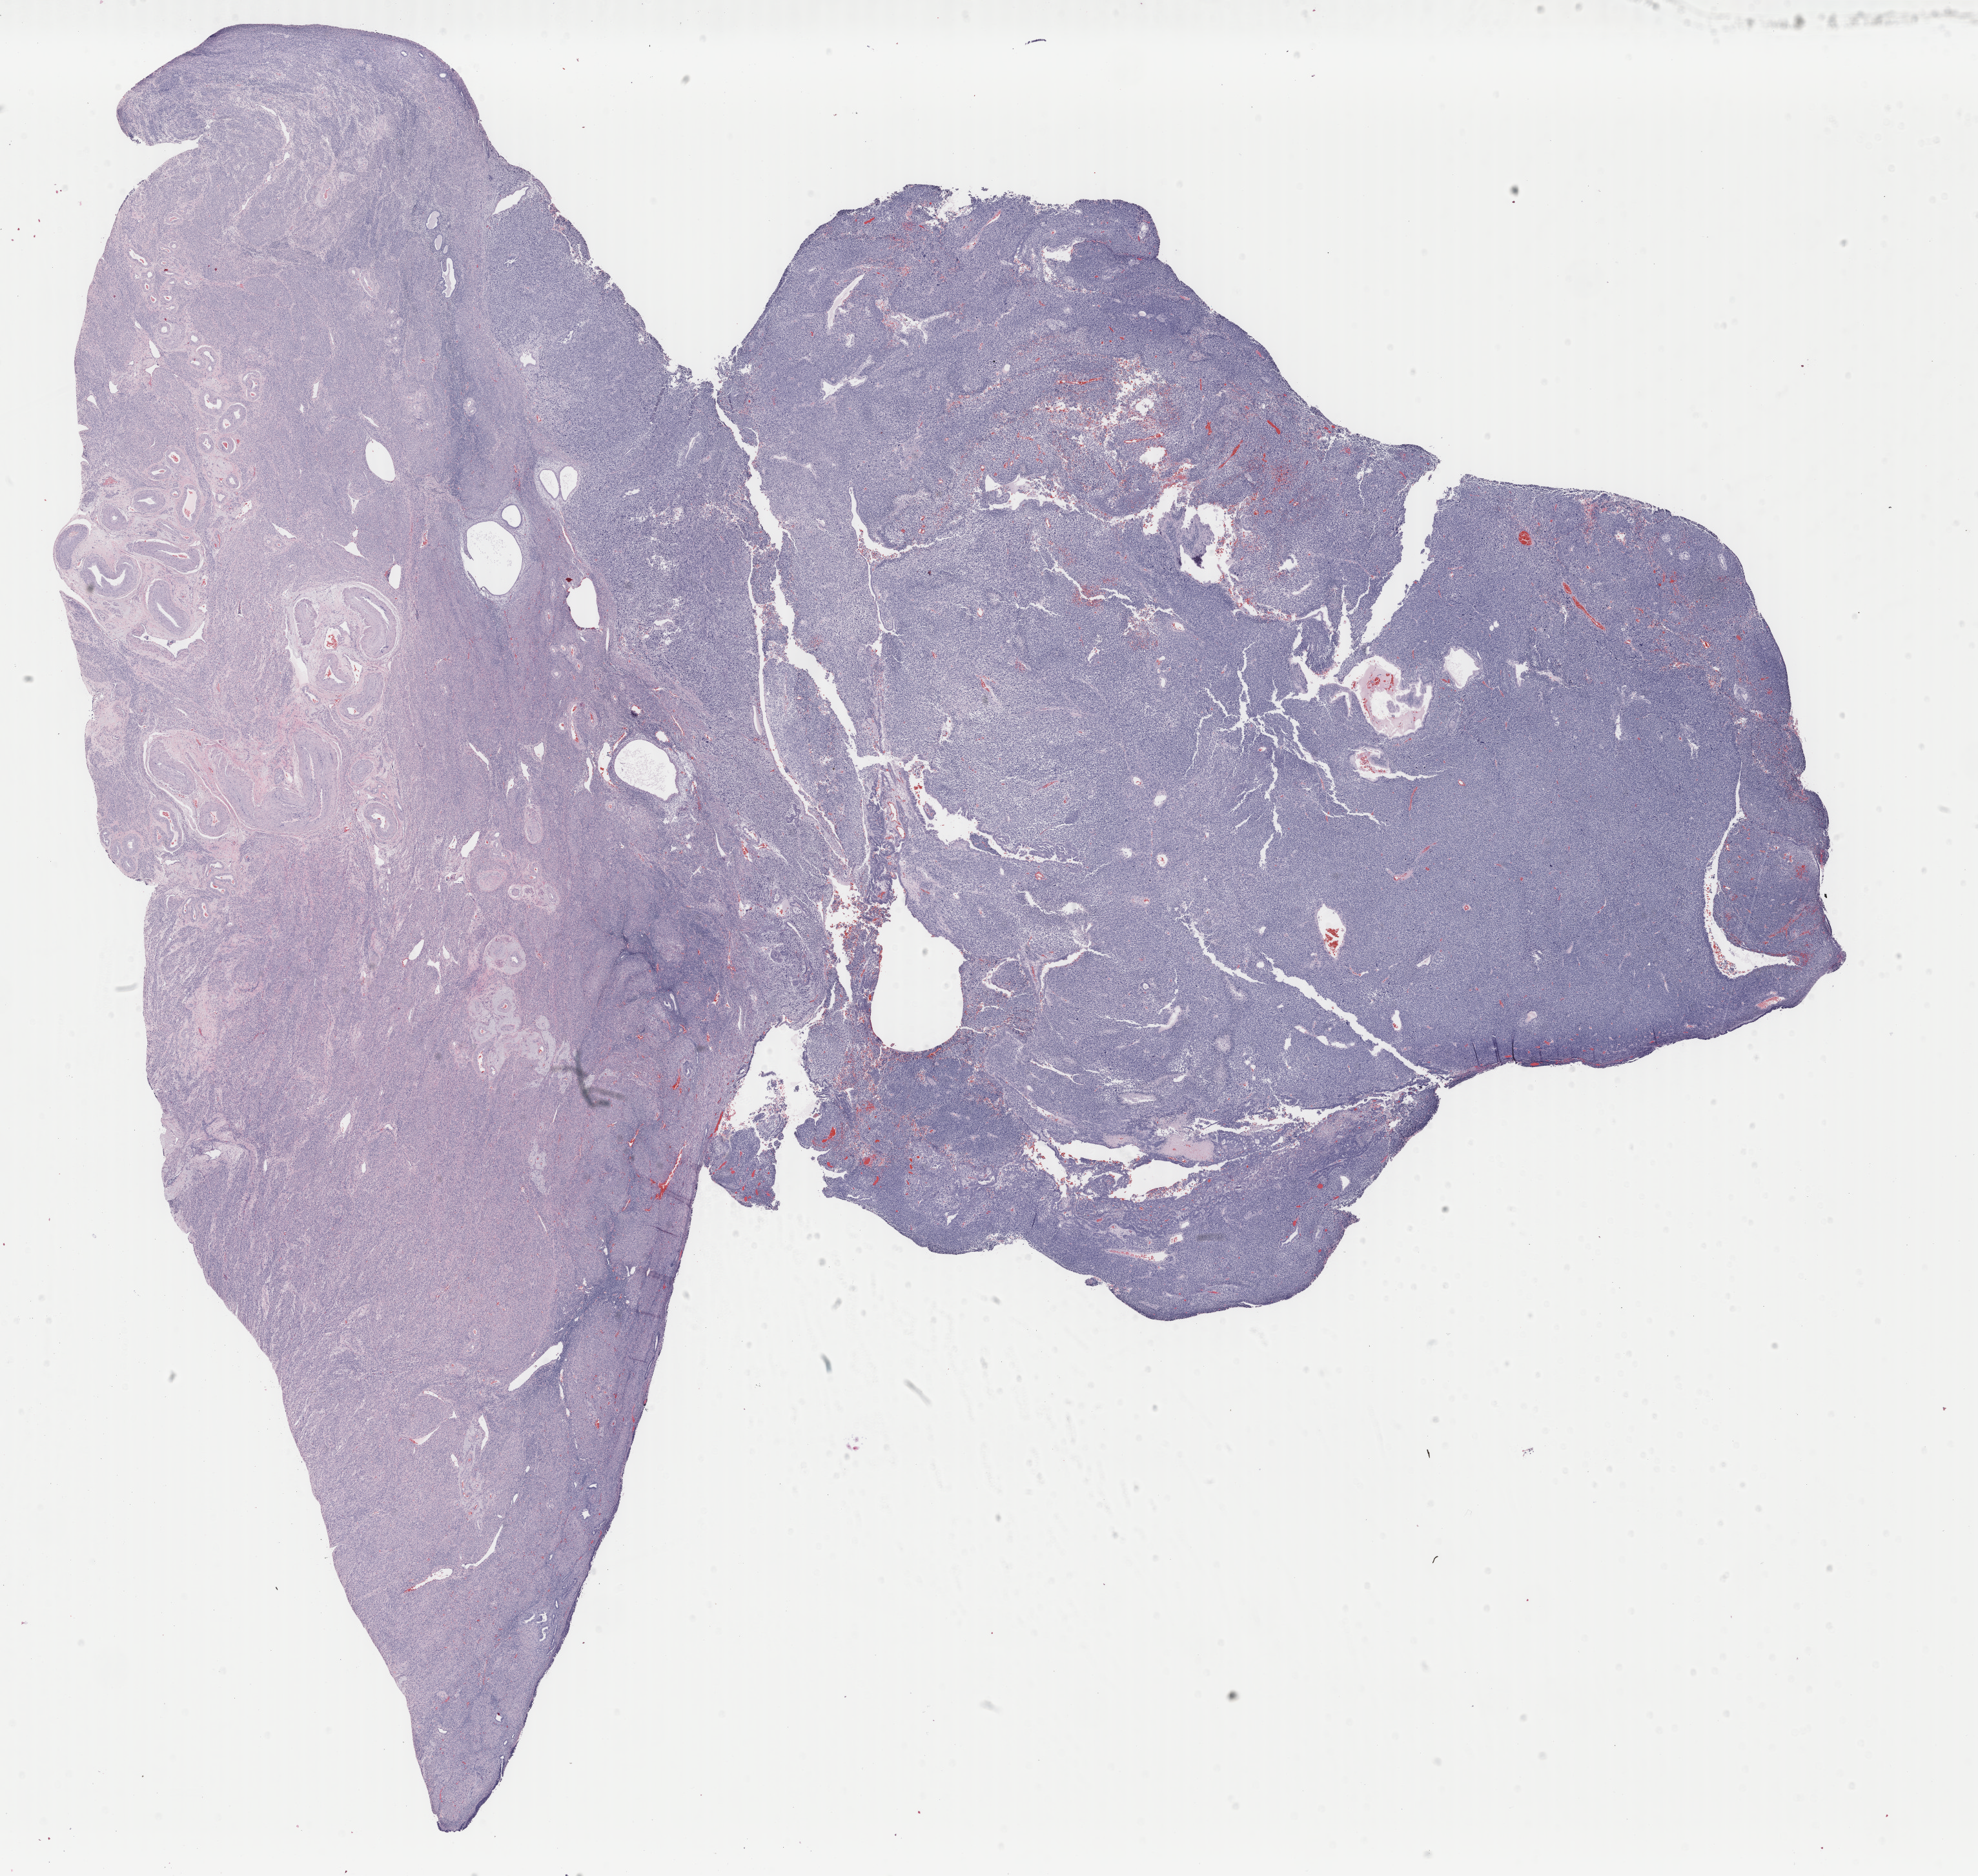
Digitized H&E-stained tissue section (whole slide) — shown as a low-resolution overview of the whole scanned area (about 24.3 x 23.1 mm, acquisition: 40x scan). Formalin-fixed paraffin-embedded (FFPE) diagnostic section. Uterus, primary tumour sample. Patient: female, age at initial diagnosis 62 years.
Histologic diagnosis: Mullerian mixed tumor. FIGO stage: IA.